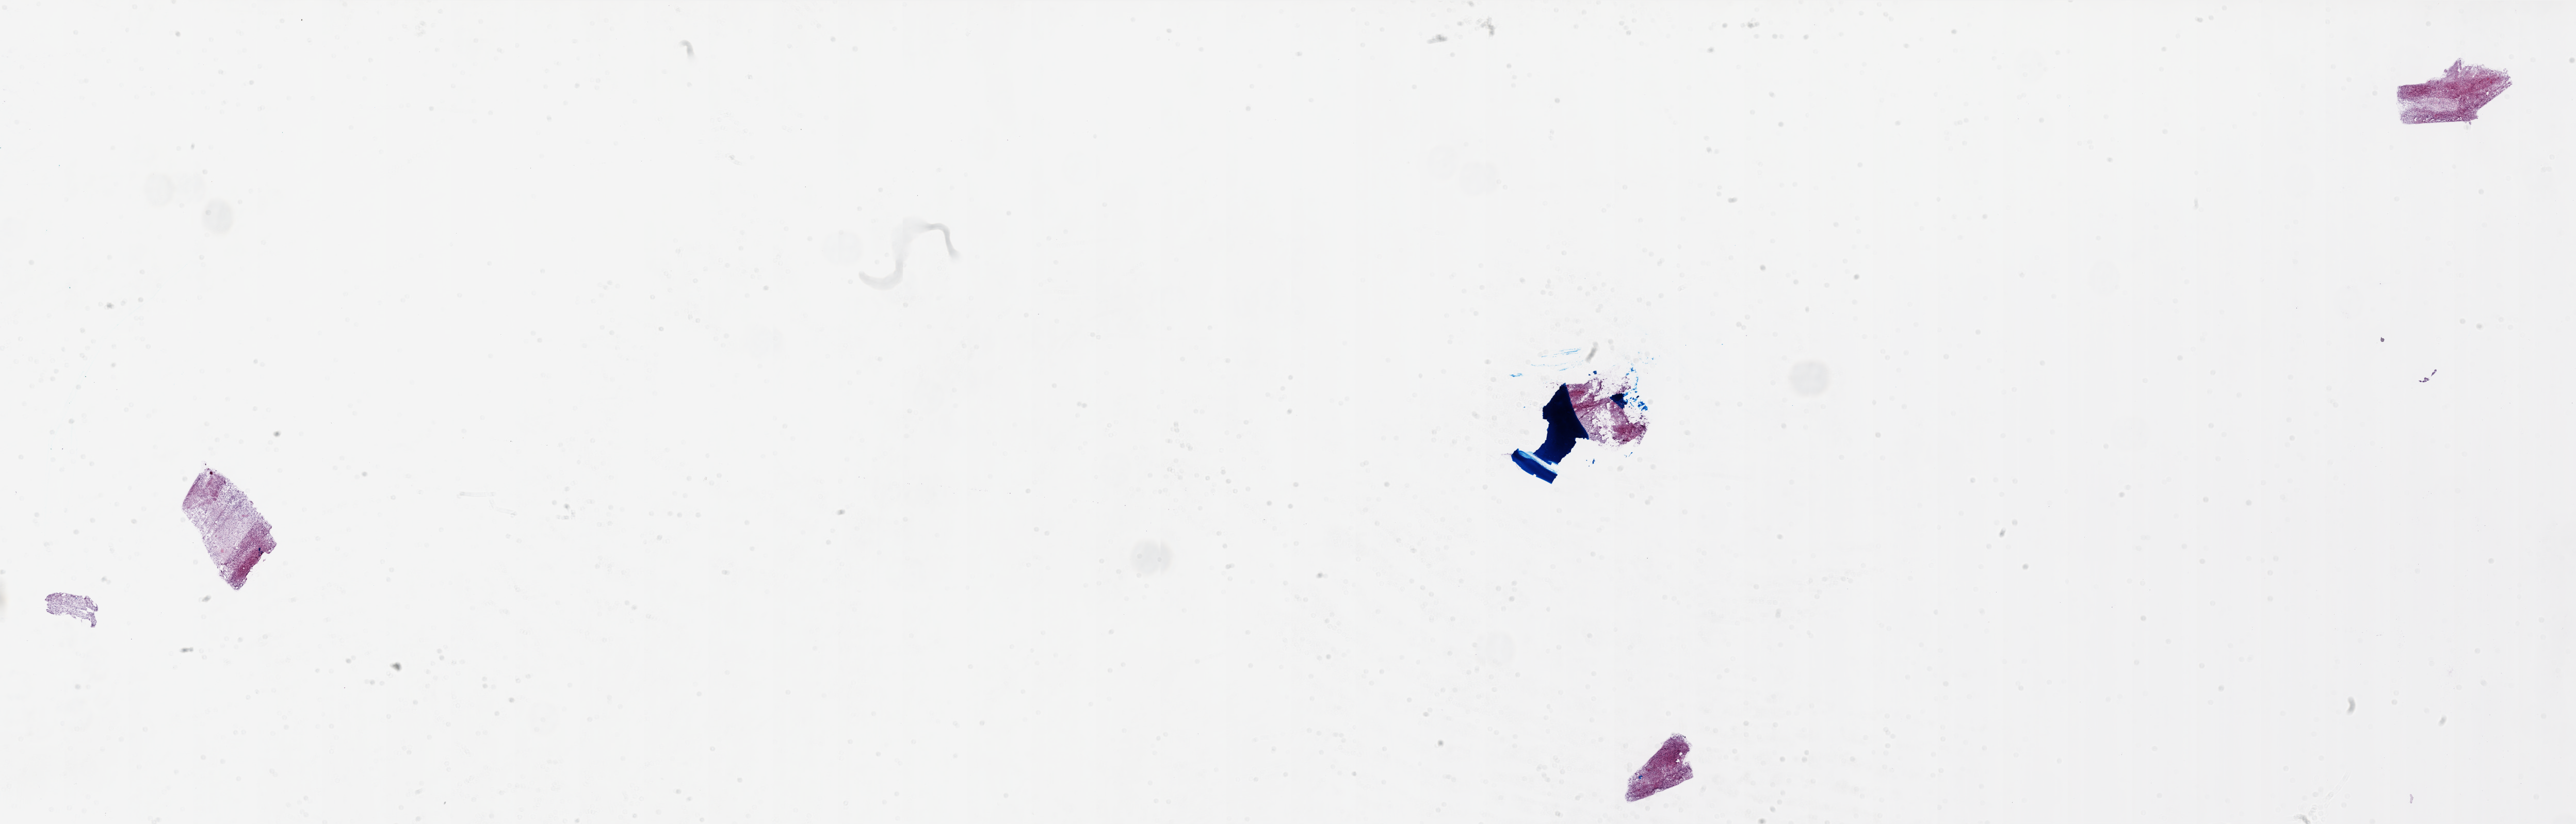
Digitized Hematoxylin and eosin (H&E) stained tissue section (whole slide) — low-resolution overview of the scanned area, about 40.0 x 12.8 mm, frozen section from the top of the tissue portion, primary tumour sample from the brain. Female patient; age at initial diagnosis 51 years. Composition of this section per pathologist review: tumour cells 60%, tumour nuclei 95%, normal cells 0%, stromal cells 0%, necrosis 40%.
• pathologic diagnosis: Glioblastoma